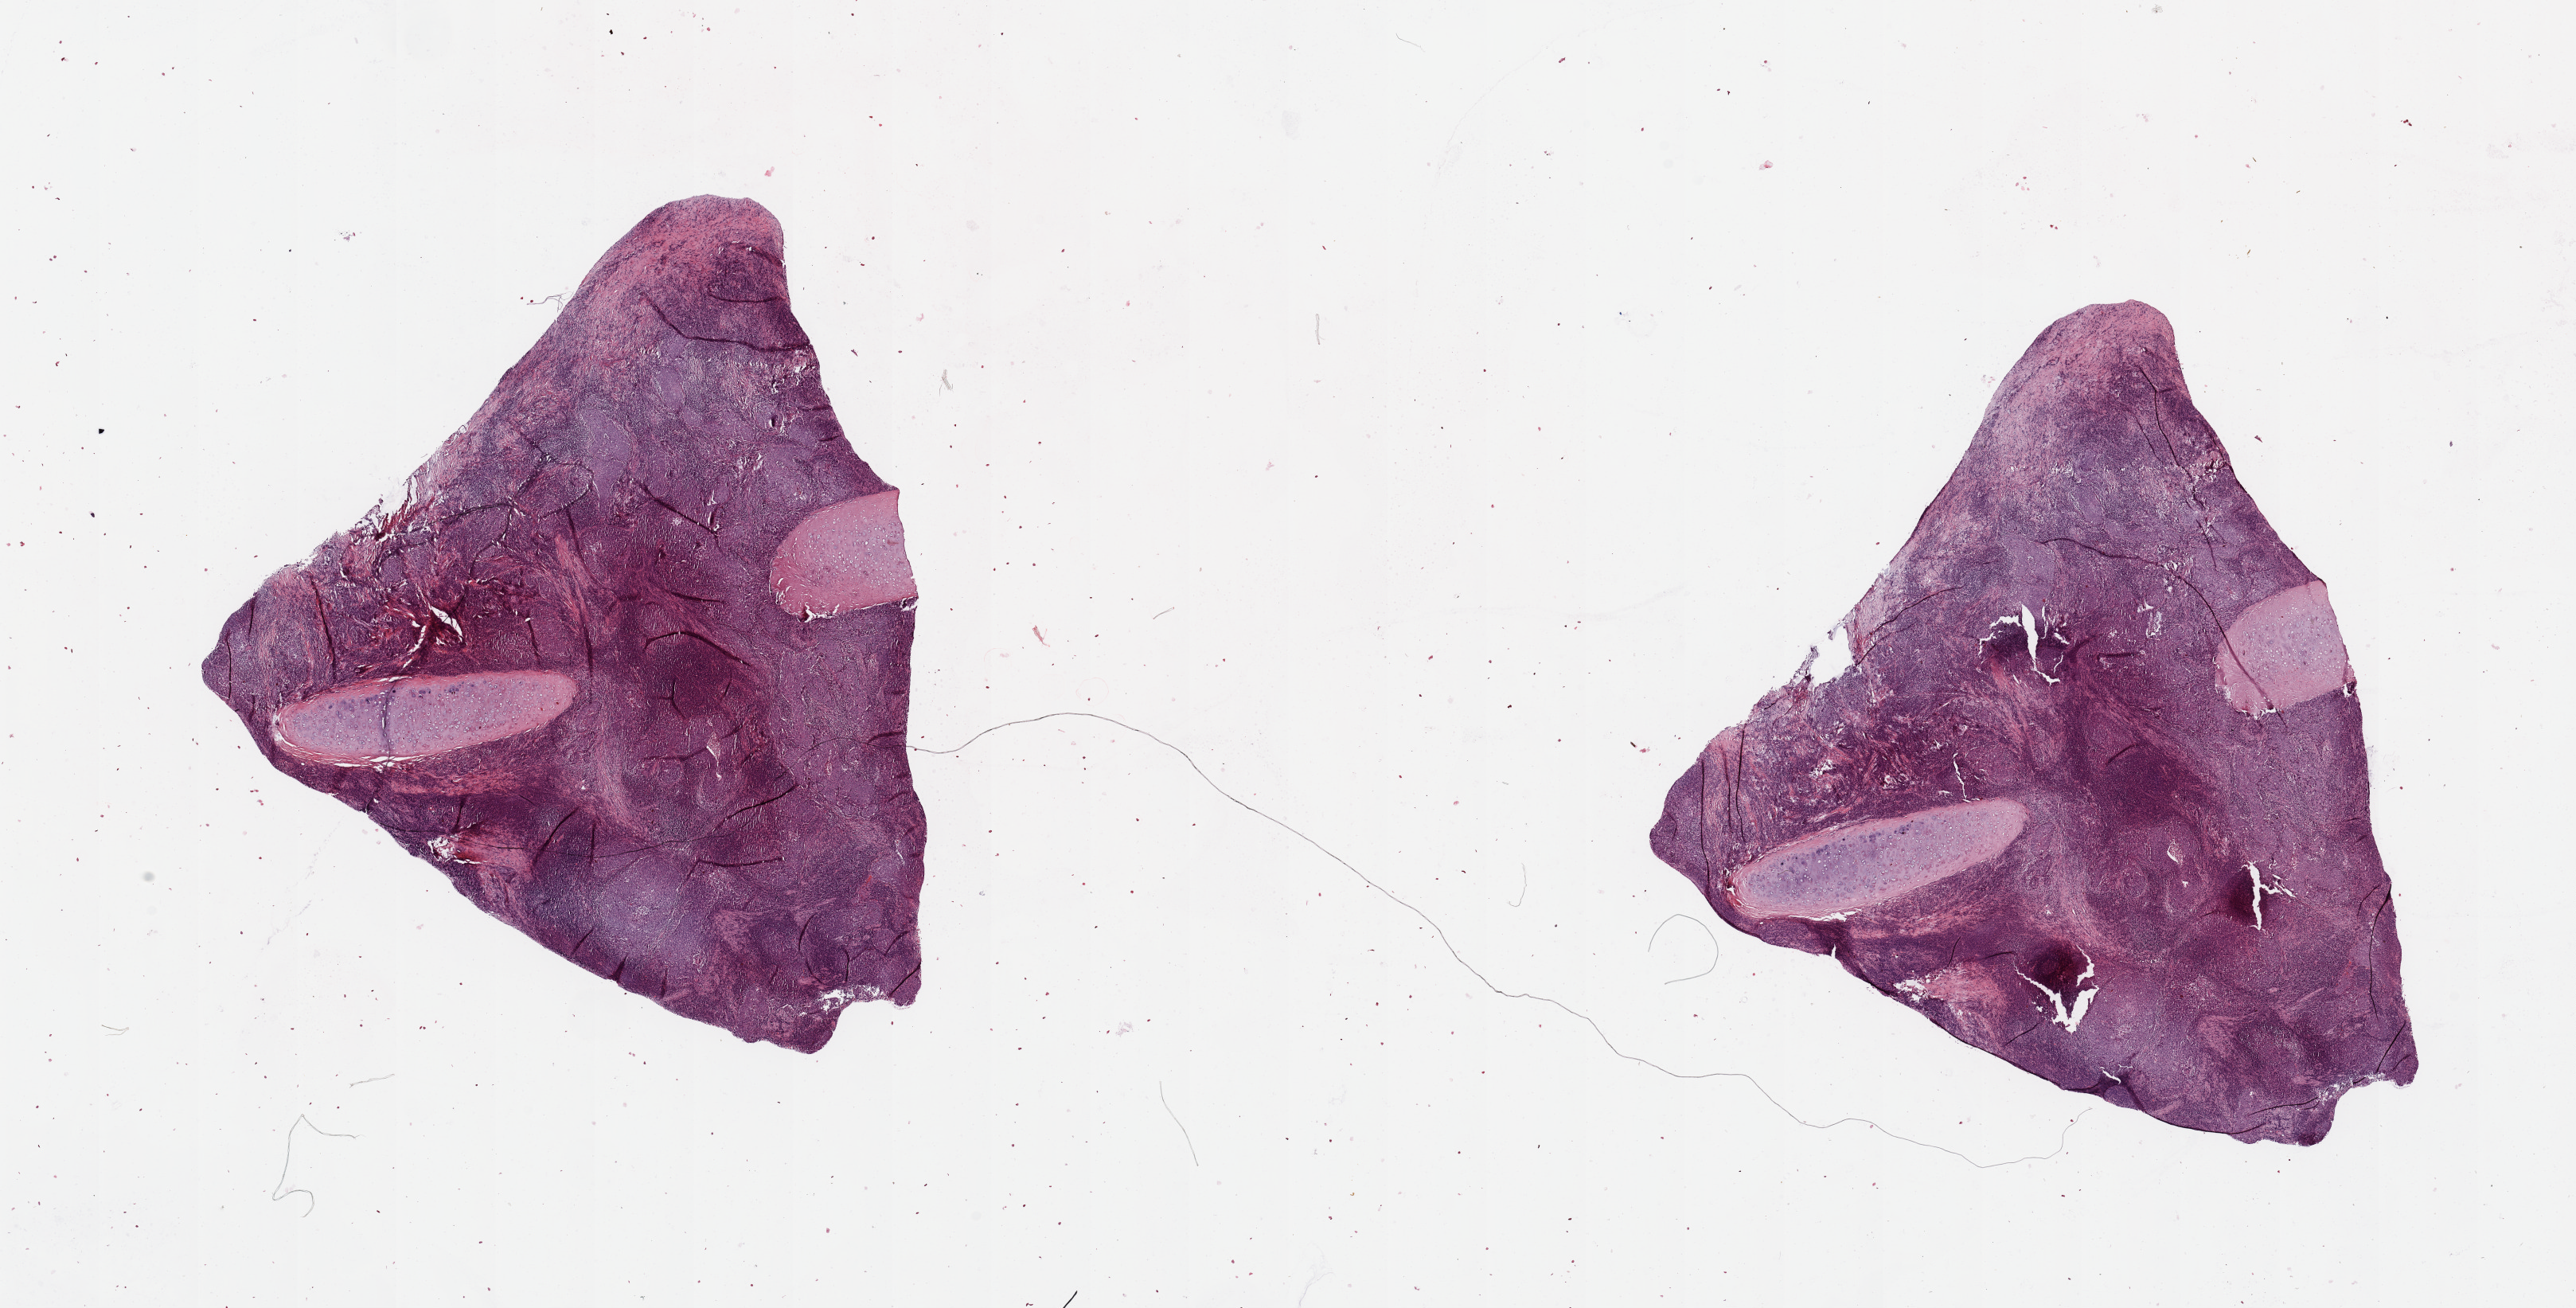
H&E-stained whole-slide image, whole scanned area (about 25.6 x 13.0 mm) shown as a low-resolution overview; tumour tissue sample, lung. Male, 66 y/o. Histologic grade: G3 (poorly differentiated).
AJCC pathologic stage: IIA. Histologic diagnosis: Squamous cell carcinoma, NOS.